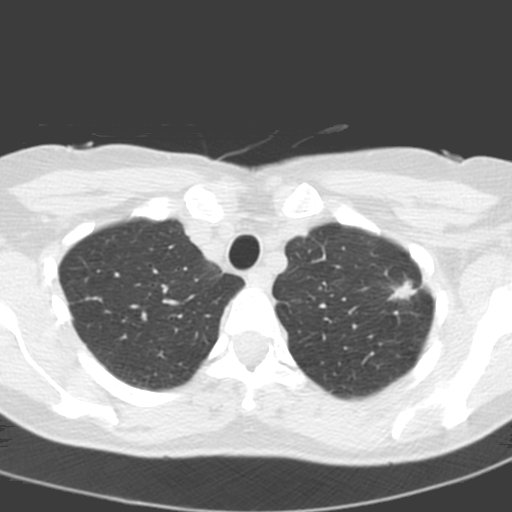
Low-dose screening chest CT, one axial slice; position 161 of 193 along the scan axis; lung window (W 1500 / L -600 HU); 512 × 512 image matrix, field of view 272 × 272 mm.
Structures marked on this image (manually delineated by an expert):
- lesion 1 (tumor, upper lobe of left lung): bounding box <390,280,417,300> (left, top, right, bottom; pixels)